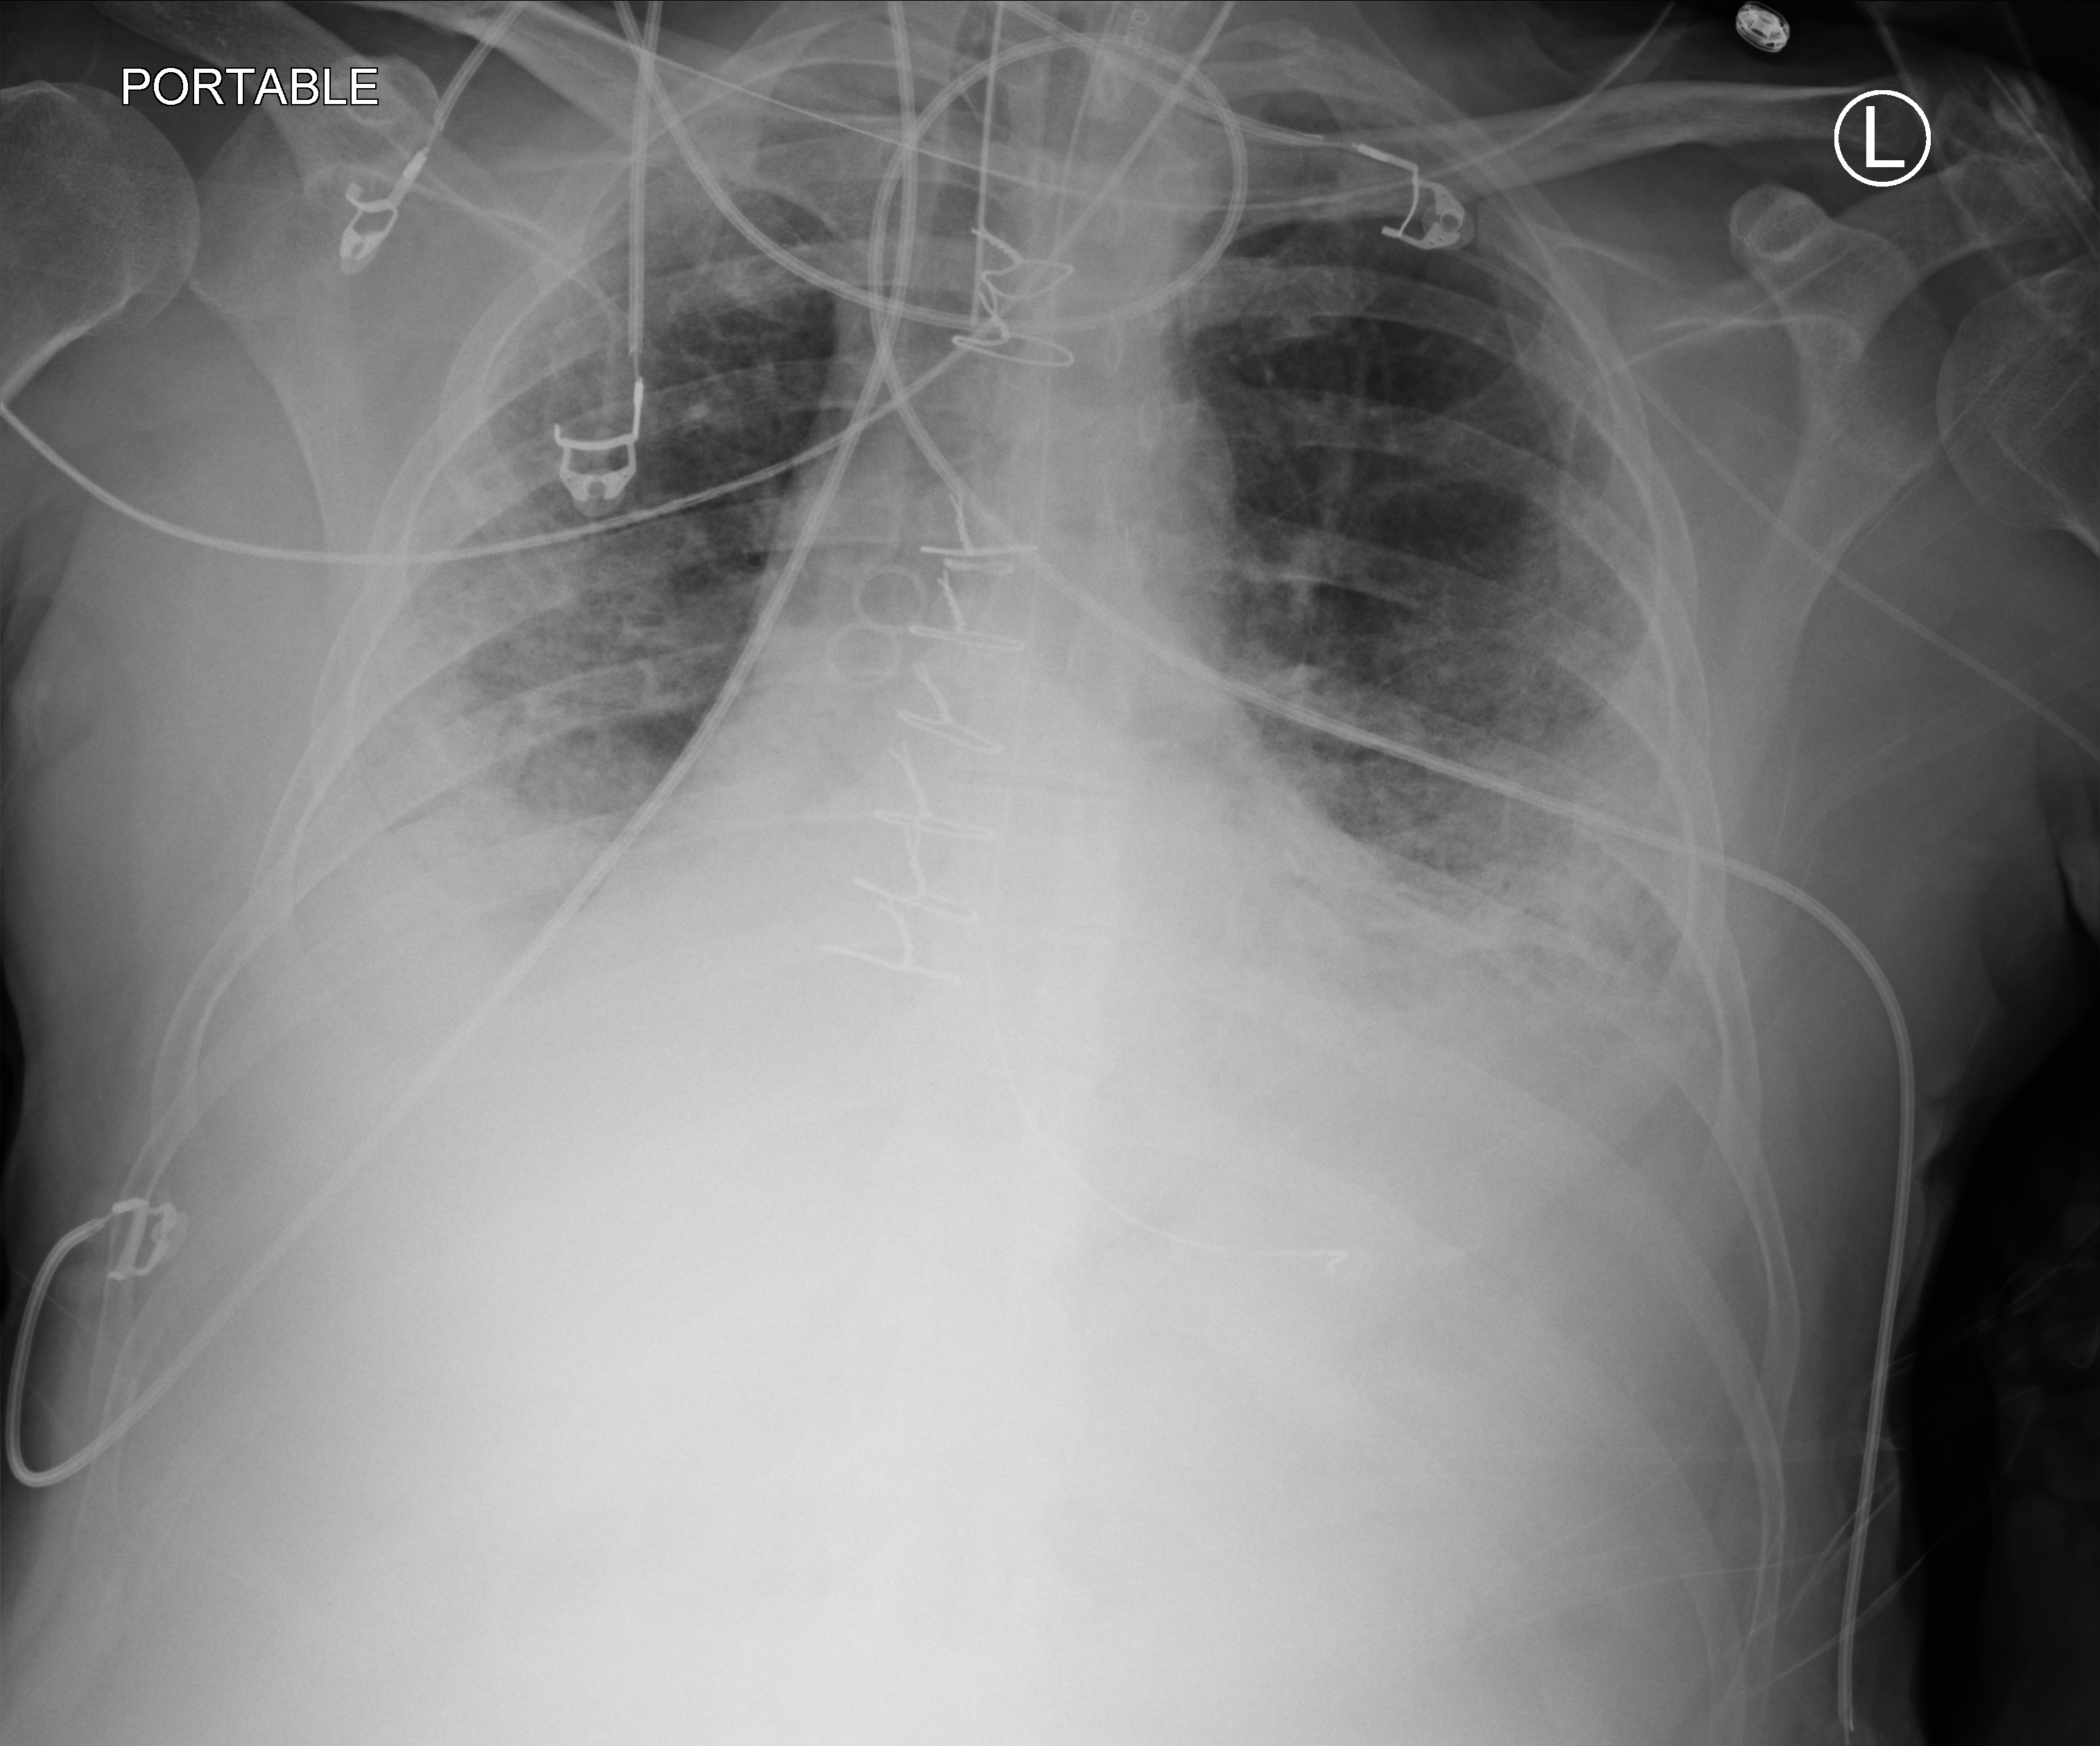
Chest X-ray (portable). Patient hospitalised with COVID-19; male, aged 18–59 years.
Admission-level facts for this patient (not findings on this image; timing relative to this image not recorded): diabetes (admission record): yes; mechanically ventilated during this hospital stay: yes; admitted to intensive care during this hospital stay: yes.